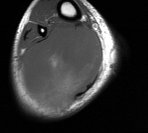
MRI of an extremity soft-tissue mass, one axial slice; slice 38 of 76 in the series (ordered by position); MR volume resampled by the dataset authors to the PET/CT grid (not the native acquisition matrix); 148 × 133 image matrix, field of view 145 × 130 mm. Male patient. From the clinical record (not read from this slice): histological type: liposarcoma - round cell; grade: high; site of the primary tumour: right calf.
Structures marked on this image (expert contour drawn on MRI and transferred to this co-registered scan by the dataset authors):
- gross tumour volume (mass): box from (x=20, y=26) to (x=101, y=111) px